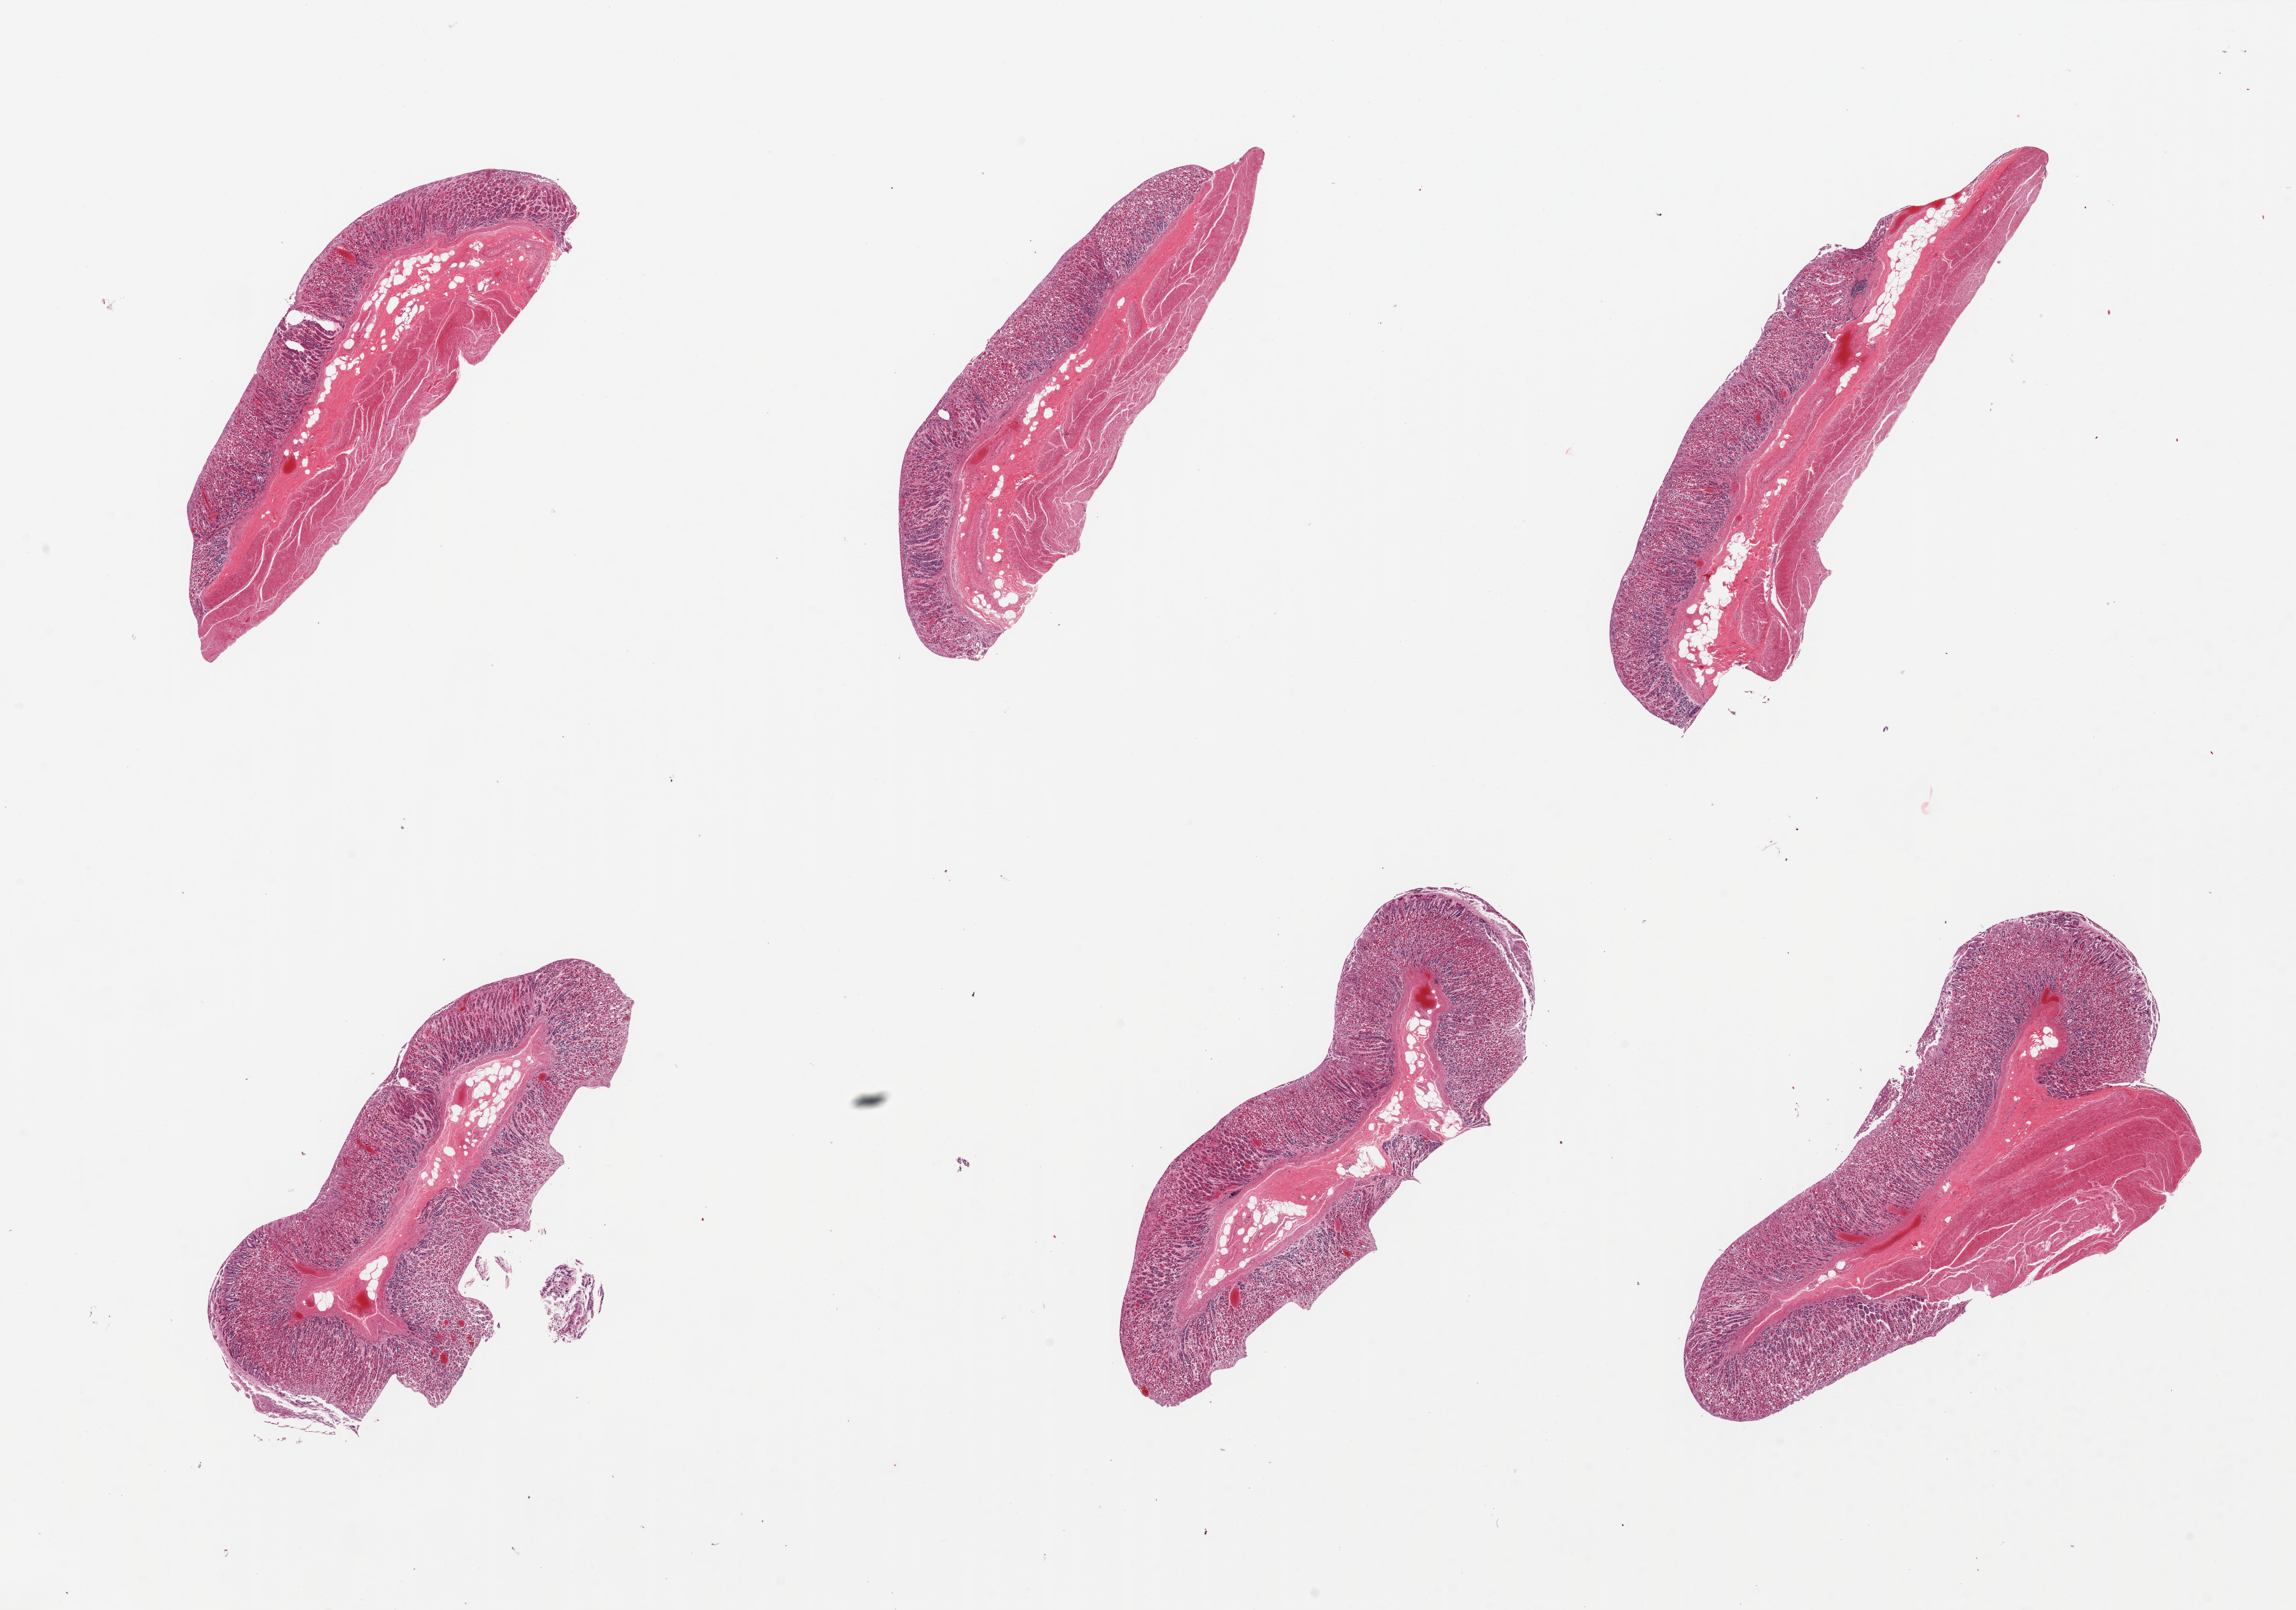
Digitized H&E-stained section, whole scanned area (about 28.5 x 20.0 mm) shown as a low-resolution overview; PAXgene-fixed paraffin-embedded (PFPE) section; sampled site (target tissue): stomach; tissue donor sample. Donor: female.
* reviewer comment on this tissue sample: 6 pieces, mucosa is up to ~1mm thick but moderately autolyzed